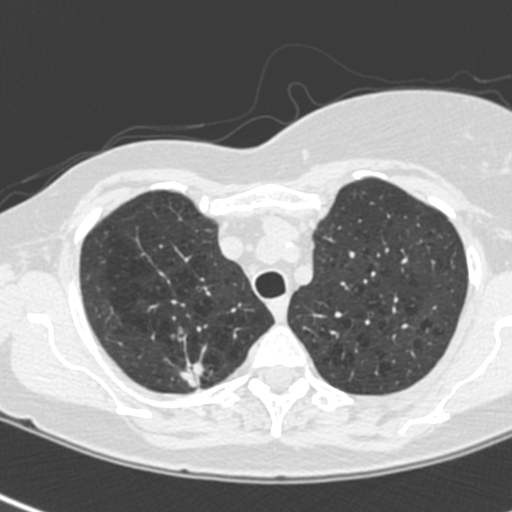
Low-dose screening chest CT, one axial slice. Lung window (W 1500 / L -600 HU). 512 × 512 image matrix.
Outlined on this slice (expert manual segmentation):
- lesion 1 (tumor, upper lobe of right lung): bounding box <180,362,204,387> (left, top, right, bottom; pixels)